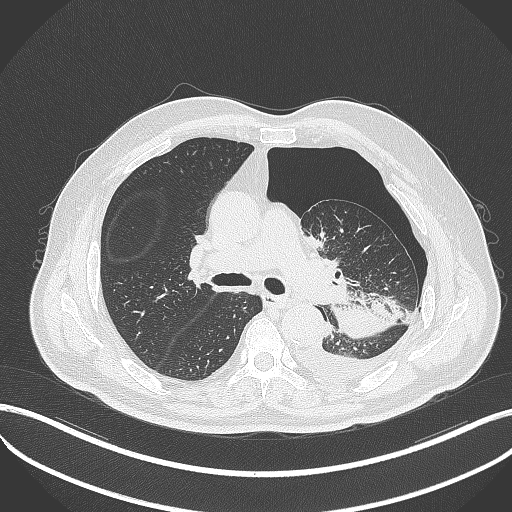
Chest CT, one axial slice. Slice 318 of 464 in the series (ordered by position). Reconstruction kernel B70f. 120 kVp. Lung window (W 1500 / L -600 HU). 1 mm slice thickness. 512 × 512 image matrix, field of view 400 × 400 mm. Male patient, age 76 years. From the clinical record (not read from this slice): clinical TNM (as recorded): T3 N0 M1b.
Annotated regions visible in this slice (rectangle marked by the reading radiologist):
- lung tumour (recorded histology: adenocarcinoma): bounding box [x1, y1, x2, y2] px = [325, 297, 394, 338]